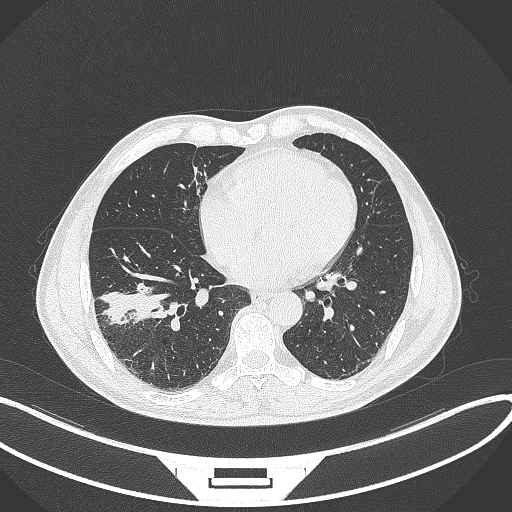
Chest CT, one axial slice; slice 139 of 364 in the series (ordered by position); 120 kVp; lung window (W 1500 / L -600 HU); 512 × 512 image matrix, field of view 400 × 400 mm. Patient: male, 58 years. Case-level facts recorded for this patient, not image findings: clinical TNM (as recorded): T3 N0 M0.
Outlined on this slice (rectangle marked by the reading radiologist):
- lung tumour (recorded histology: squamous cell carcinoma): bounding box [x1, y1, x2, y2] px = [96, 288, 167, 328]